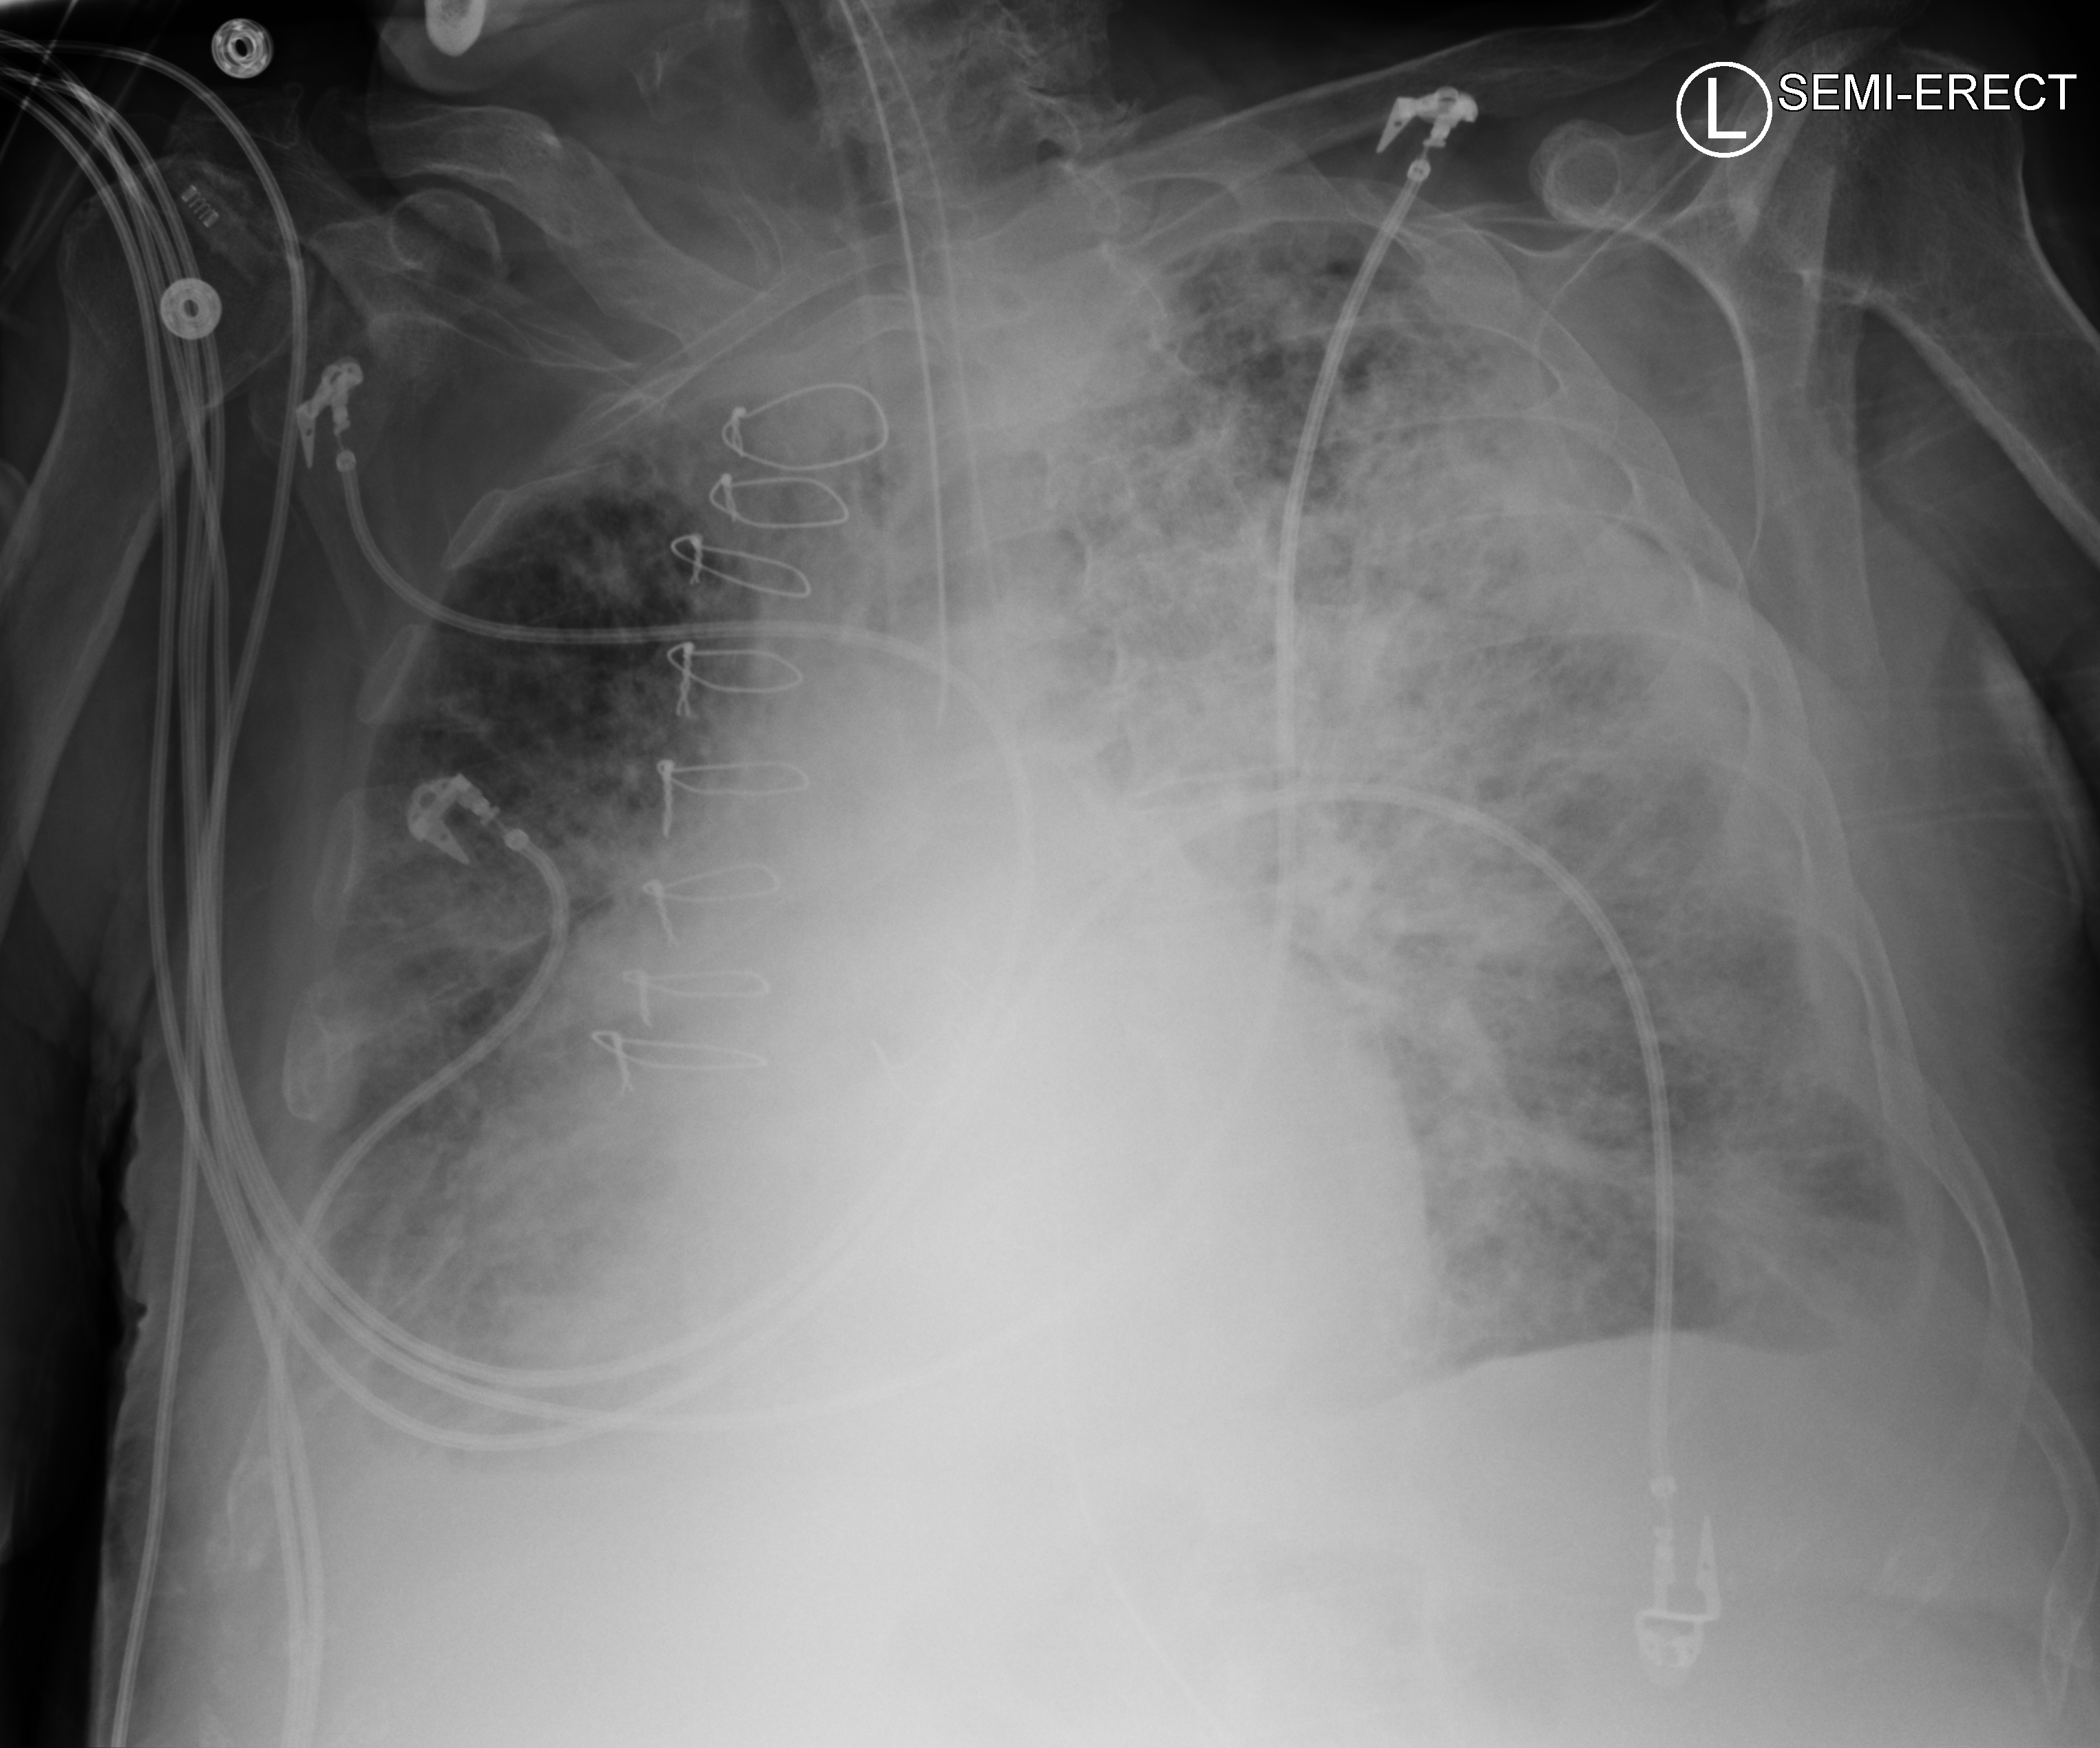
Bedside chest radiograph (computed radiography), anteroposterior (AP) projection. Patient hospitalised with COVID-19; male, aged 75–90 years.
Hospital-stay facts (about this admission, not read from this image; timing relative to this image not recorded): length of hospital stay: 40 days; admitted to intensive care during this hospital stay: yes.